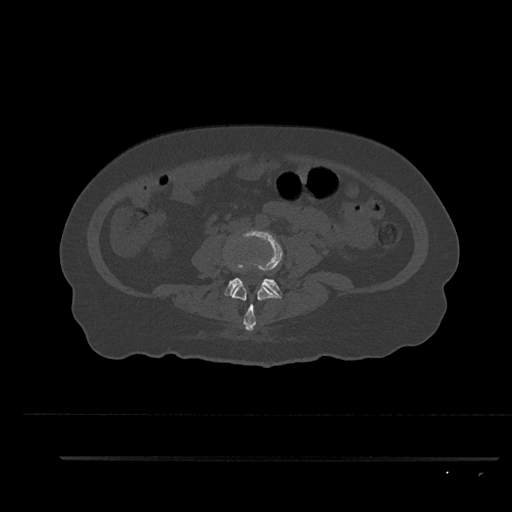
CT including the spine, one axial slice; slice 50 of 797 in the series (ordered by position); reconstruction kernel Br40s/3; 120 kVp; bone window (W 1800 / L 400 HU); 512 × 512 image matrix. Patient: female, 44 years. From the clinical record (not read from this slice): primary cancer: renal; vertebrae with lytic lesions (as recorded): L1.
Structures marked on this image (semi-automatic segmentation, software-assisted and operator-edited):
- L3 vertebra: box from (x=232, y=285) to (x=281, y=331) px
- L4 vertebra: (x=224, y=230)–(x=283, y=298)